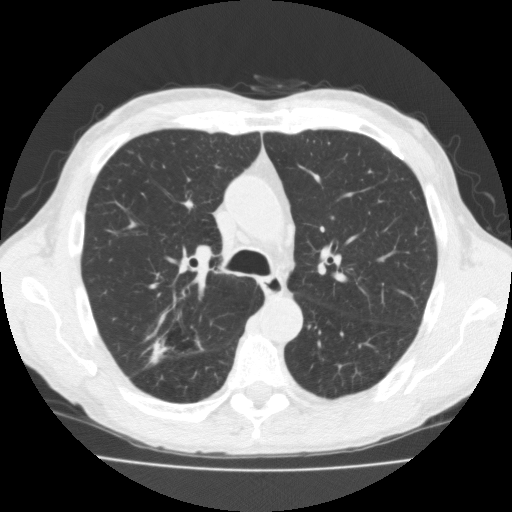
Low-dose screening chest CT, one axial slice. Position 119 of 181 along the scan axis. Reconstruction kernel FC10. 120 kVp. Lung window (W 1500 / L -600 HU). 2 mm slice thickness. 512 × 512 image matrix, field of view 350 × 350 mm.
Structures marked on this image (expert manual segmentation):
- lesion 1 (tumor, upper lobe of right lung): box from (x=150, y=342) to (x=166, y=364) px